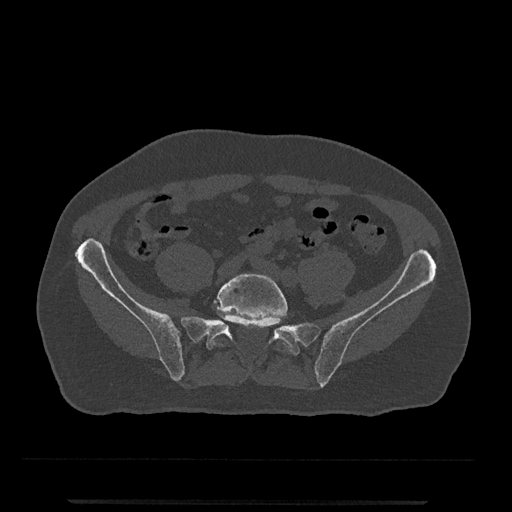
CT including the spine, one axial slice; slice 43 of 797 in the series (ordered by position); 120 kVp; bone window (W 1800 / L 400 HU); 0.5 mm slice thickness; 512 × 512 image matrix. Patient: male, 63 years. From the clinical record (not read from this slice): primary cancer: prostate.
Structures marked on this image (semi-automatic segmentation, software-assisted and operator-edited):
- L5 vertebra: bounding box <209,274,289,352> (left, top, right, bottom; pixels)